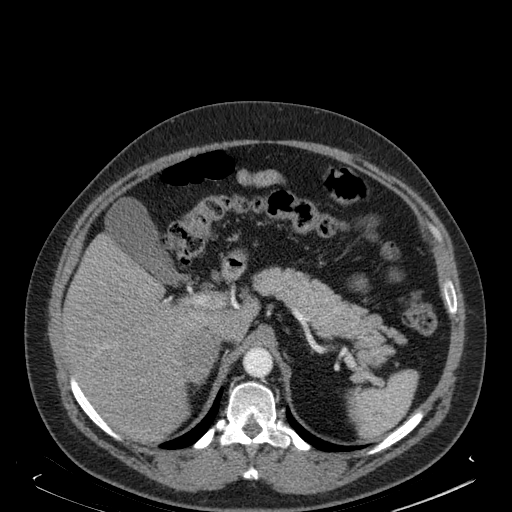
Contrast-enhanced abdominal CT, one axial slice; slice 126 of 181 in the series (ordered by position); soft-tissue window (W 400 / L 40 HU); 1.5 mm slice thickness; 512 × 512 image matrix, field of view 405 × 405 mm. Male patient. From the clinical record (not read from this slice): diagnosis: adrenocortical carcinoma; tumour side: right adrenal; tumour size at pathology: 7.5 cm; Ki-67 index: 25 %; stage (as recorded): 4.
Outlined on this slice (semi-automatically segmented with operator editing):
- mass: bounding box (x1, y1, x2, y2) in pixels: (183, 328, 217, 381)